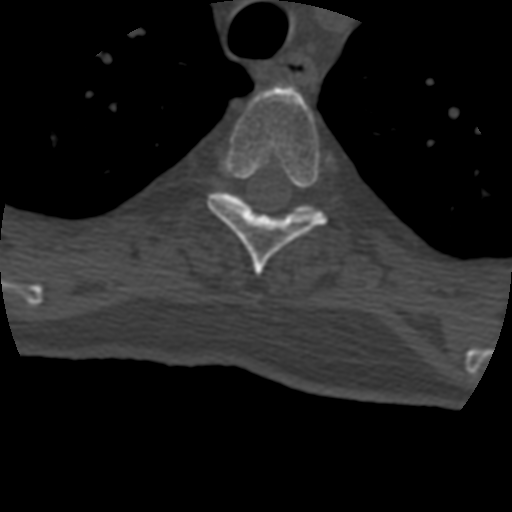
CT including the spine, one axial slice; slice 335 of 399 in the series (ordered by position); reconstruction kernel STANDARD; bone window (W 1800 / L 400 HU); 1.25 mm slice thickness; 512 × 512 image matrix, field of view 160 × 160 mm. Patient age 69 years. Case-level facts recorded for this patient, not image findings: primary cancer: prostate.
Annotated regions visible in this slice (semi-automatic segmentation, software-assisted and operator-edited):
- T4 vertebra: bounding box <207,86,328,277> (left, top, right, bottom; pixels)
- T5 vertebra: <227,194,309,215>